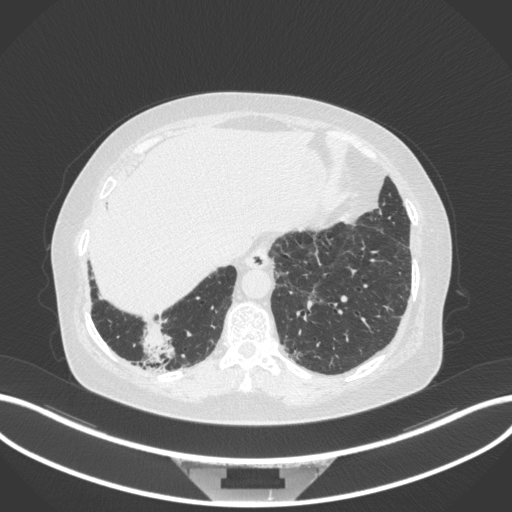
Chest CT, one axial slice; slice 26 of 303 in the series (ordered by position); lung window (W 1500 / L -600 HU); 1 mm slice thickness; 512 × 512 image matrix. Patient: female, 65 years. Case-level facts recorded for this patient, not image findings: clinical TNM (as recorded): T2b N1 M0.
Structures marked on this image (rectangle marked by the reading radiologist):
- lung tumour (recorded histology: adenocarcinoma): bounding box [x1, y1, x2, y2] px = [134, 322, 181, 368]